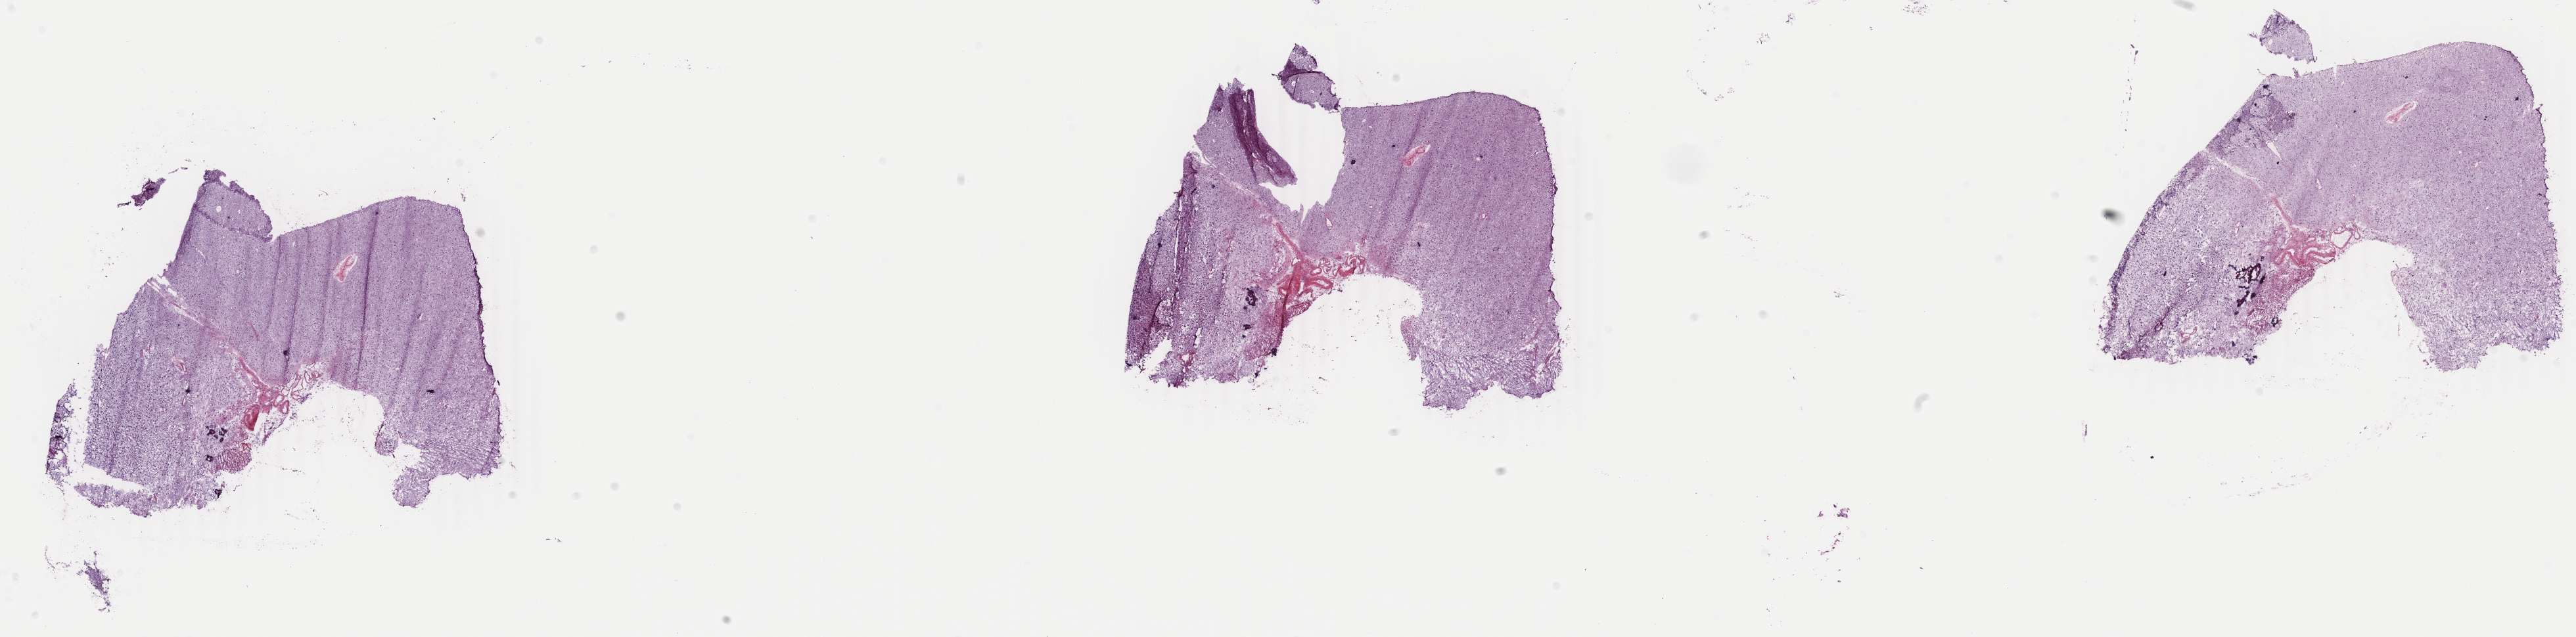
Whole-slide histology image, H&E, shown as a low-resolution overview of the whole scanned area (about 31.2 x 7.7 mm); frozen section; sample: primary tumour, brain. Male, age 35 years at initial diagnosis. Histologic grade: G2 (moderately differentiated). Pathologist review of this section (percent, as recorded): tumour cells 40%, tumour nuclei 80%, normal cells 10%, stromal cells 50%, necrosis 0%. Infiltration values recorded for this section: lymphocyte infiltration 0%, monocyte infiltration 0%, neutrophil infiltration 0%.
Laterality: midline. Diagnosis: Oligodendroglioma, NOS.